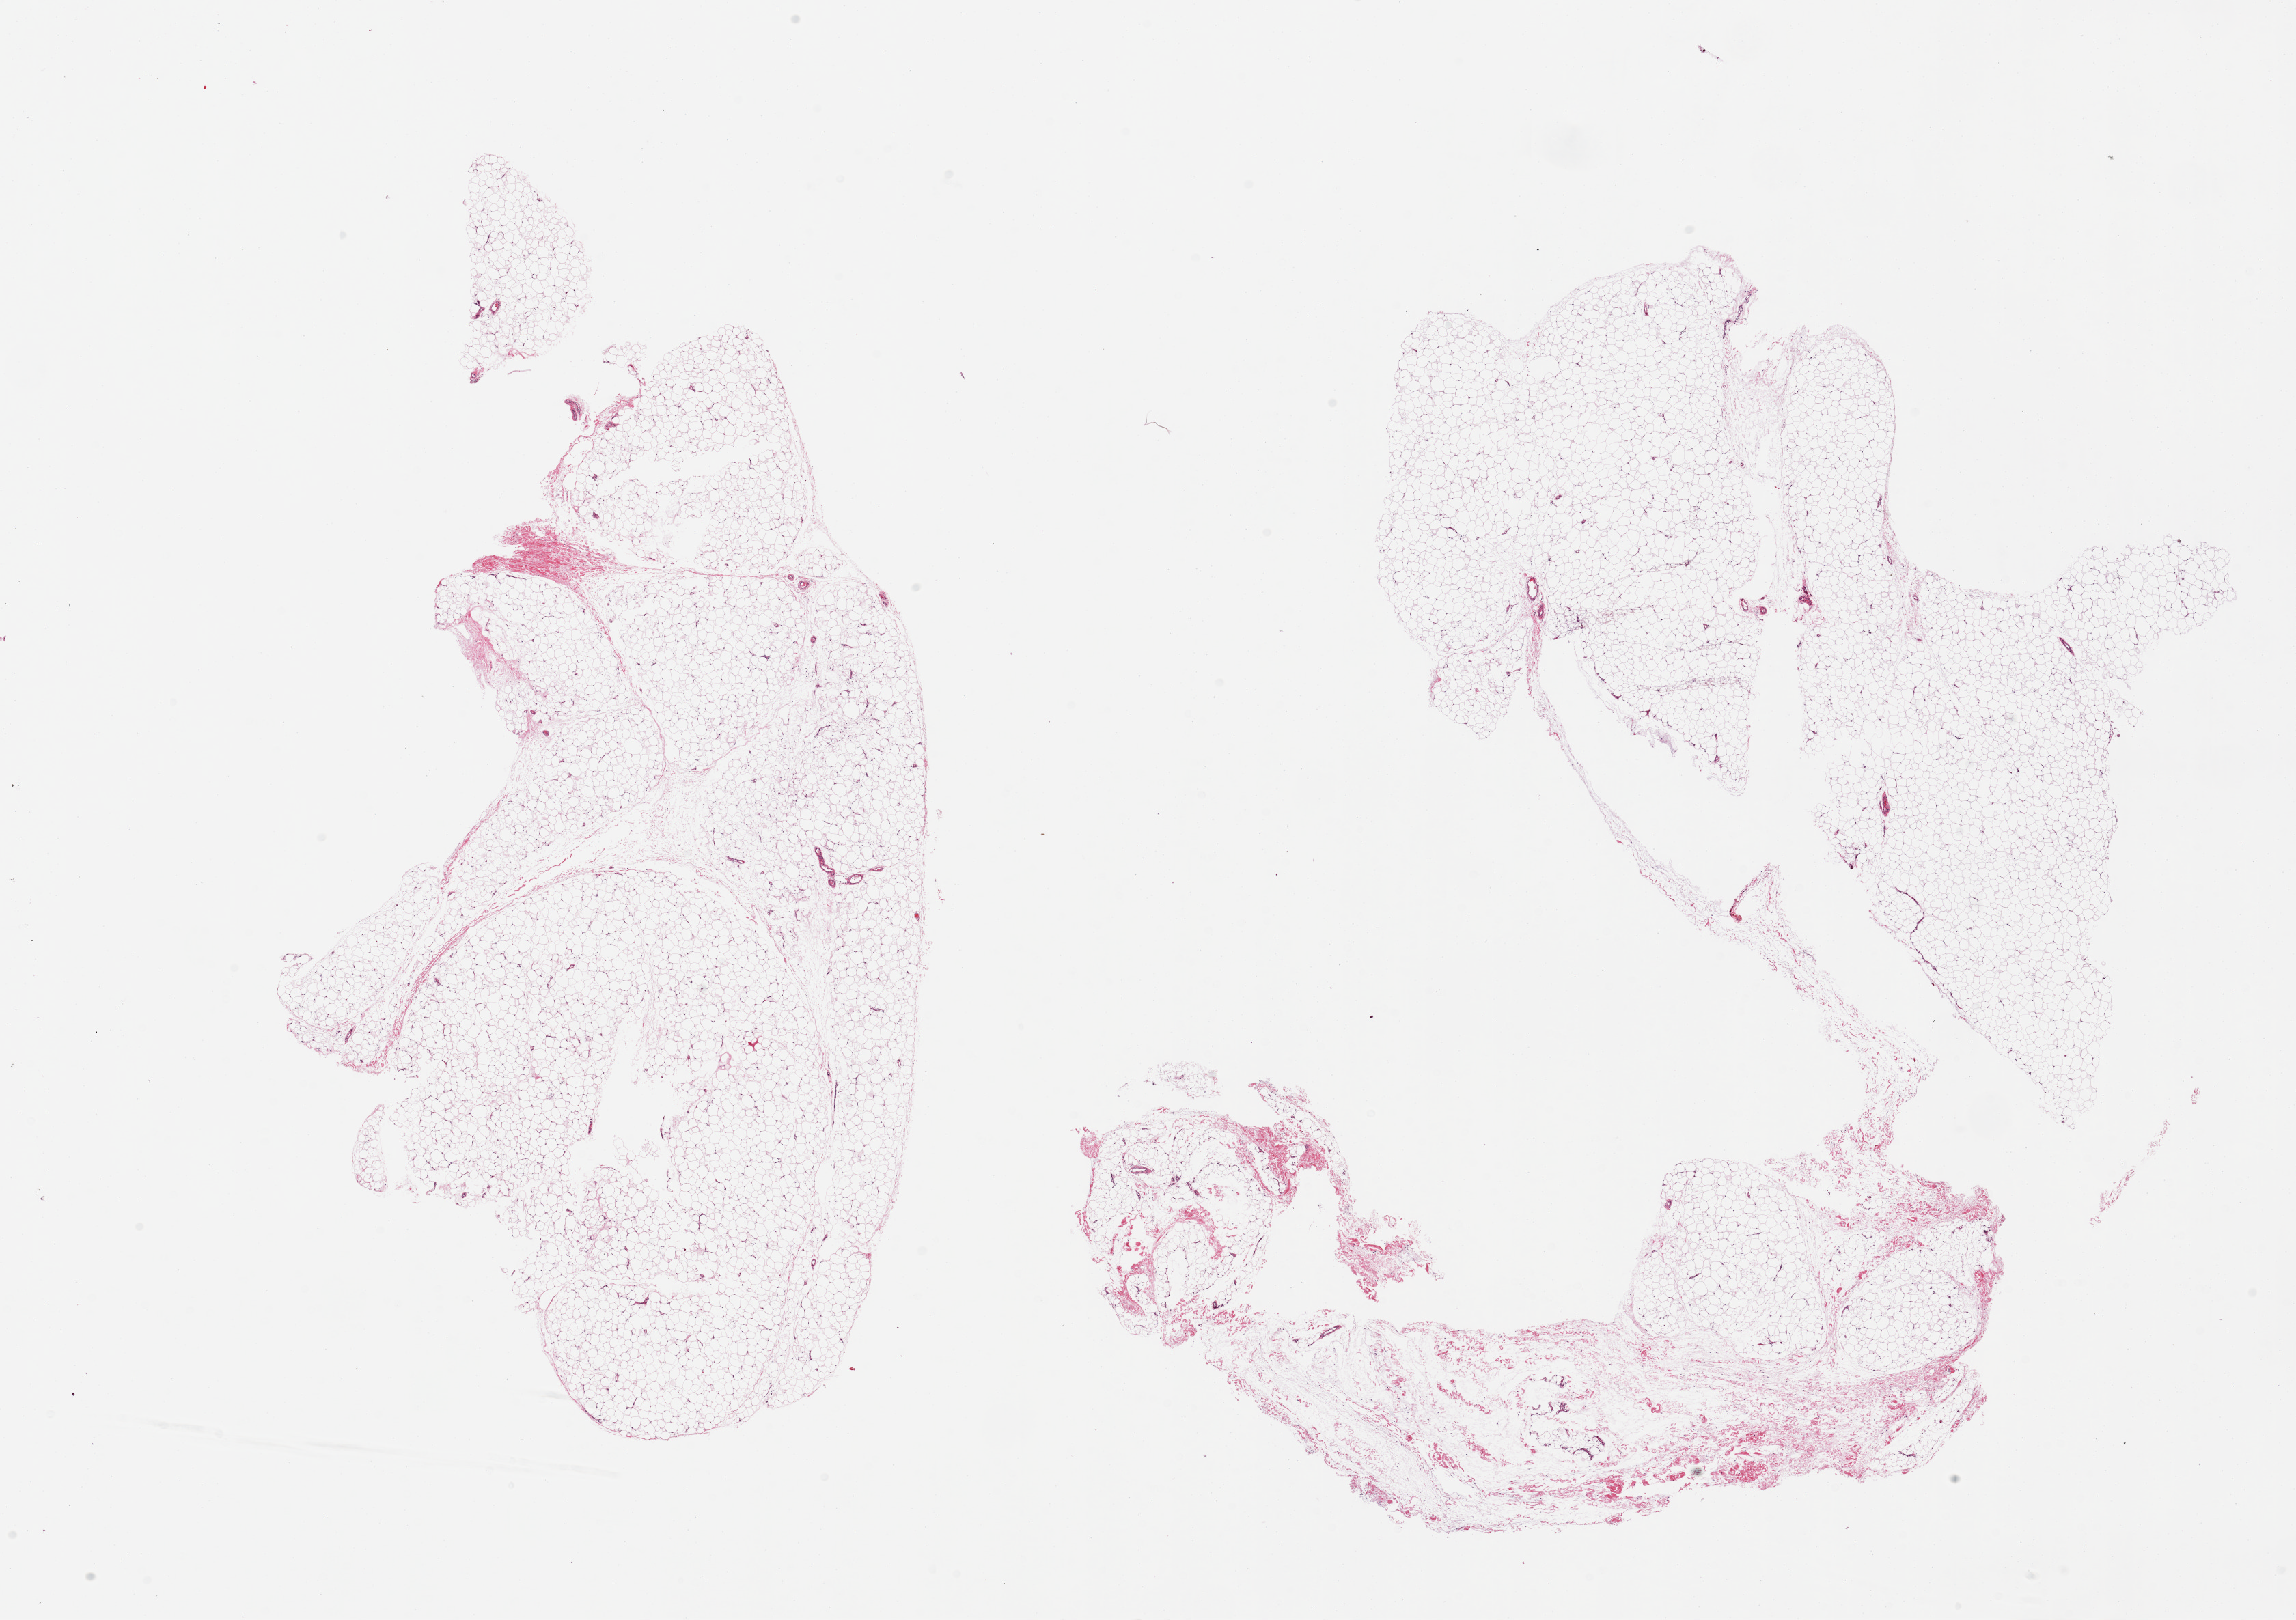
H&E whole-slide image — shown as a low-resolution overview of the whole scanned area (about 26.6 x 18.8 mm, from a 20x scan), PAXgene-fixed paraffin-embedded (PFPE) section, section of adipose tissue (target tissue), tissue donor sample.
Pathologist's review note for this sample: 2 pieces, minimal vascular elements/fascia, good specimen.